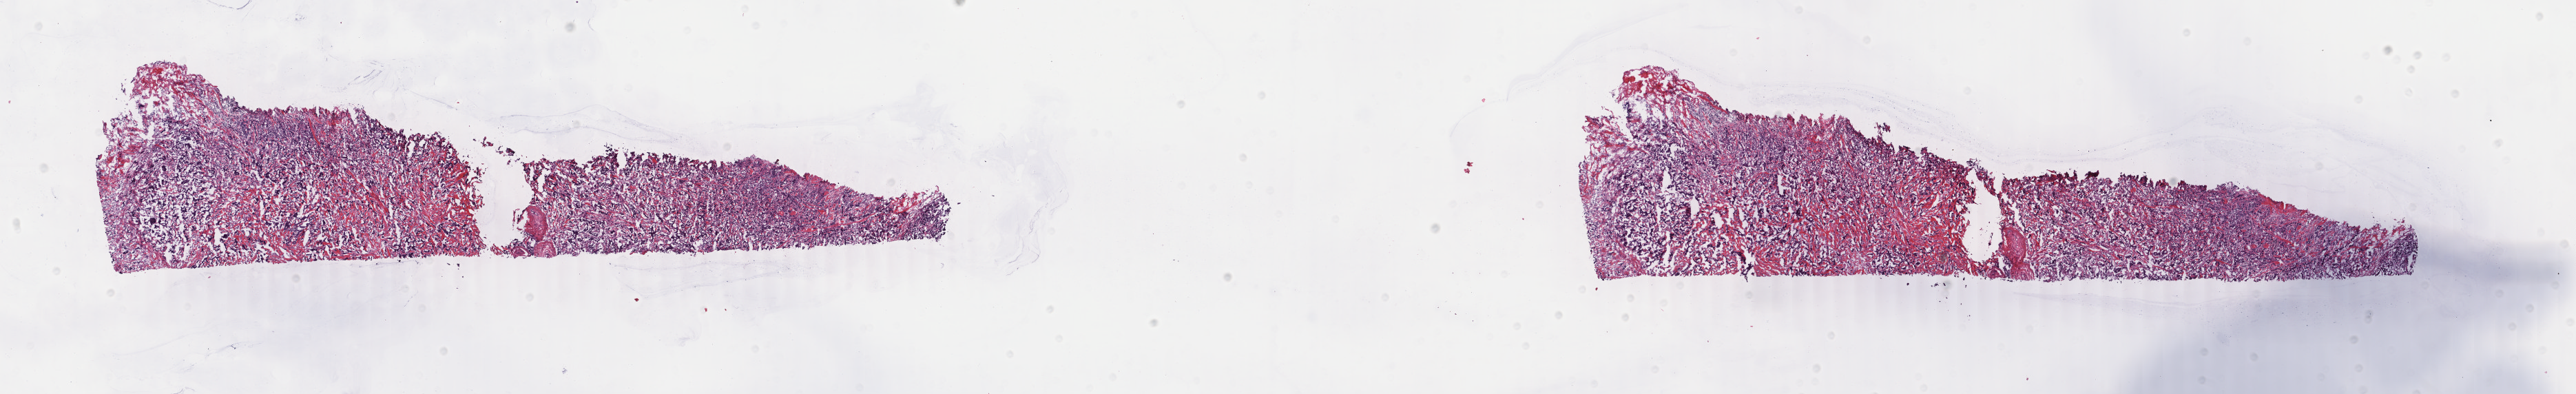
Digitized Hematoxylin and eosin (H&E) stained tissue section (whole slide), shown as a low-resolution overview of the whole scanned area (about 29.7 x 4.5 mm, from a 40x scan); frozen section from the bottom of the tissue portion; breast, primary tumour sample. Patient: female, age at initial diagnosis 40 years. Composition of this section per pathologist review: tumour cells 95%, tumour nuclei 75%, normal cells 0%, stromal cells 5%, necrosis 0%. Infiltration values recorded for this section: lymphocyte infiltration 0%, monocyte infiltration 0%, neutrophil infiltration 0%.
Lymph nodes positive (case pathology): 2 of 23 examined. Diagnosis: Infiltrating duct carcinoma, NOS. AJCC pathologic stage: IIB.